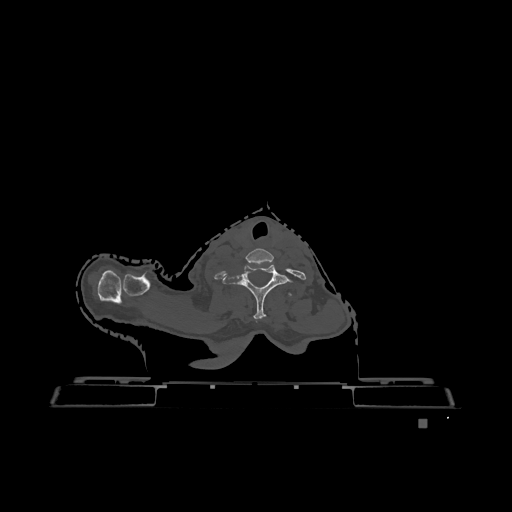
CT including the spine, one axial slice; position 1030 of 1317 along the scan axis; bone window (W 1800 / L 400 HU); 512 × 512 image matrix, field of view 500 × 500 mm. Female patient, age 74 years. Case-level facts recorded for this patient, not image findings: primary cancer: lung; vertebrae with lytic lesions (as recorded): T1, T4, T5, T6, L4, L5.
Outlined on this slice (semi-automatically segmented with operator editing):
- T1 vertebra: bounding box [x1, y1, x2, y2] px = [289, 293, 292, 296]